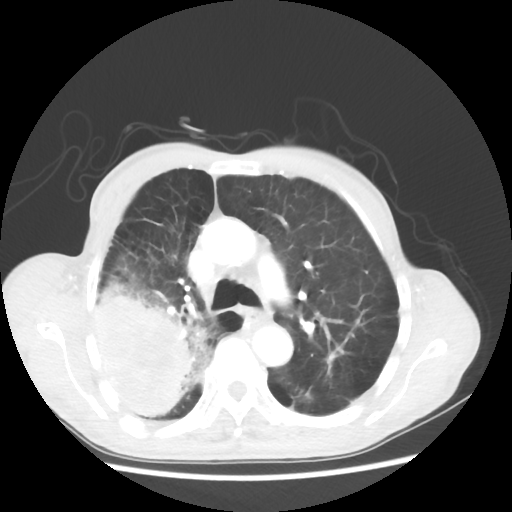
Chest CT, one axial slice. Position 36 of 58 along the scan axis. Reconstruction kernel STANDARD. 100 kVp. Lung window (W 1500 / L -600 HU). 5 mm slice thickness. 512 × 512 image matrix. Patient: male, 75 years. From the clinical record (not read from this slice): clinical TNM (as recorded): T4 N1 M1.
Annotated regions visible in this slice (rectangle marked by the reading radiologist):
- lung tumour (recorded histology: adenocarcinoma): bounding box (x1, y1, x2, y2) in pixels: (92, 267, 212, 420)